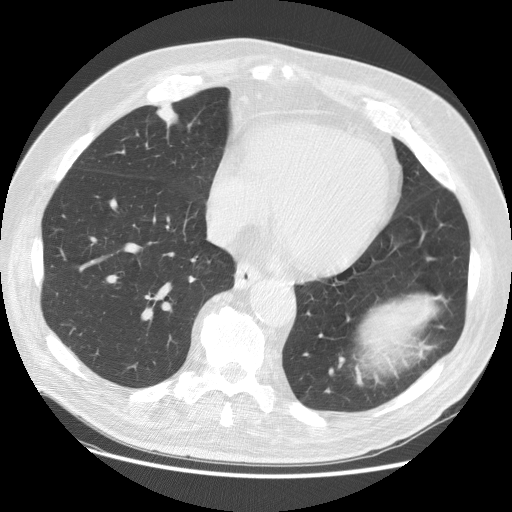
Low-dose screening chest CT, axial slice. First (baseline) screen. Lung window (W 1500 / L -600 HU). Standard (soft-tissue) reconstruction kernel (STANDARD). Slice 91 of 129 in the series. 512 × 512 image matrix. Male participant, aged 74 years at enrolment. Former smoker at enrolment.
Expert-annotated lung lesion, bounding box <149,93,187,141> (left, top, right, bottom; pixels). The exam's reader record, not a measurement of the box and not confirmed to be the same lesion: non-calcified nodule or mass ≥4 mm, right middle lobe, 24 × 24 mm, spiculated (stellate) margins, soft tissue attenuation. Lung cancer was diagnosed 296 days after this screen: papillary adenocarcinoma, NOS, right middle lobe, well differentiated (G1), stage IA (AJCC 6th edition), 20 mm at pathology.